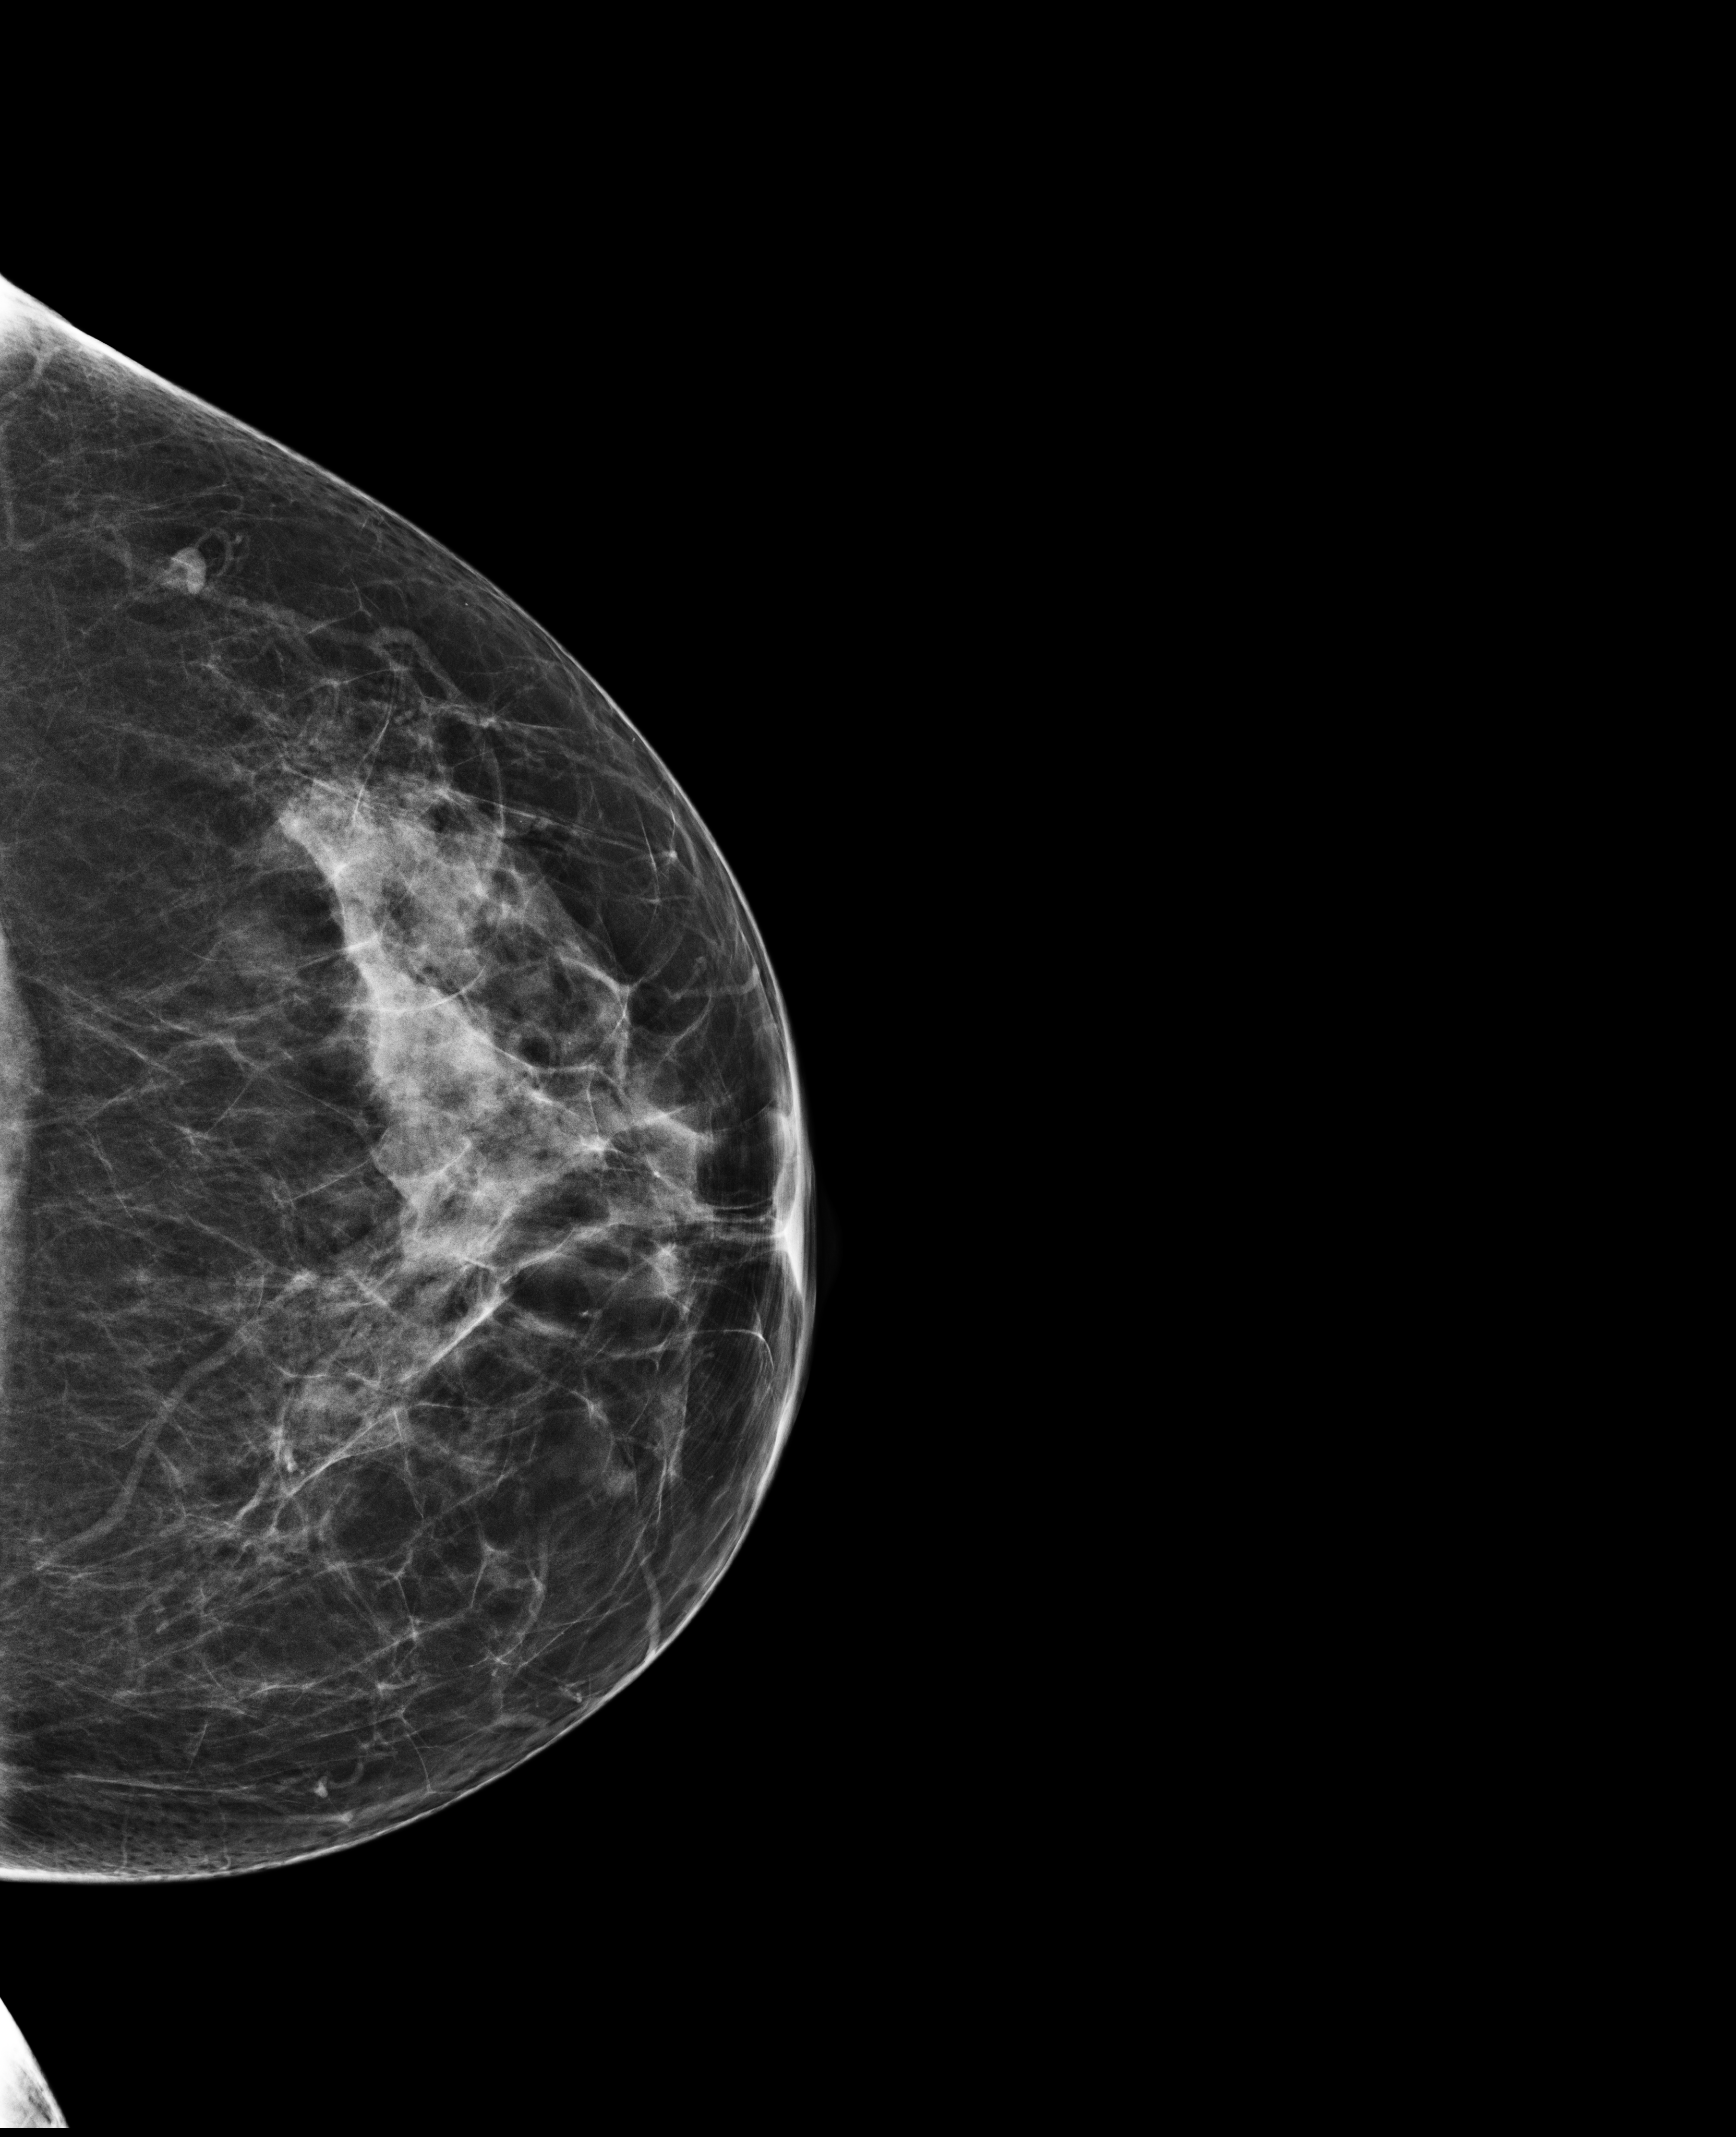
Full-field digital mammogram (FFDM), left breast, CC view, annual screening mammography examination. Female patient, age 44 years.
BI-RADS breast density category at the screening exam (both breasts, scale 1–4): 3. Final BI-RADS assessment for this screening round (tomosynthesis exam, both breasts): category 2. Recall: recalled for additional imaging after this screen.